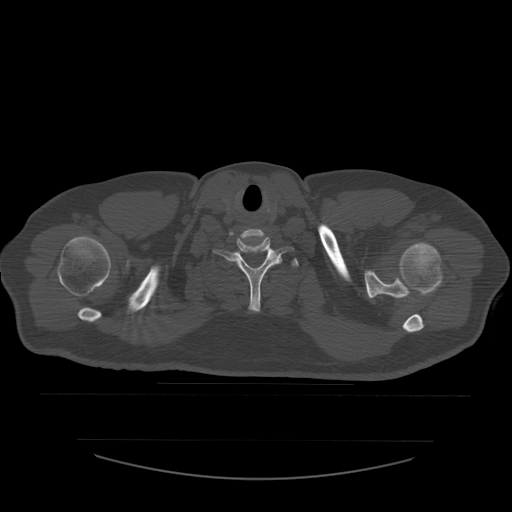
CT including the spine, one axial slice; slice 482 of 532 in the series (ordered by position); 120 kVp; bone window (W 1800 / L 400 HU); 512 × 512 image matrix, field of view 441 × 441 mm. Patient age 44 years. Case-level facts recorded for this patient, not image findings: primary cancer: soft tissue sarcoma.
Outlined on this slice (semi-automatic segmentation, software-assisted and operator-edited):
- T1 vertebra: bounding box [x1, y1, x2, y2] px = [292, 258, 299, 267]